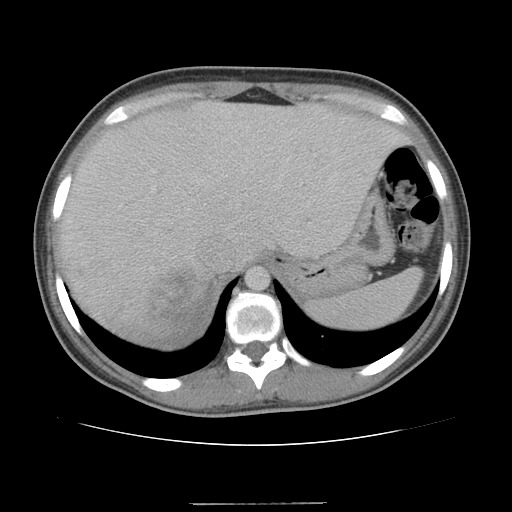
Contrast-enhanced abdominal CT, one axial slice; position 84 of 100 along the scan axis; reconstruction kernel STANDARD; intravenous contrast given; soft-tissue window (W 400 / L 40 HU); 5 mm slice thickness; 512 × 512 image matrix, field of view 360 × 360 mm. Female patient, age 21 years. Case-level facts recorded for this patient, not image findings: diagnosis: adrenocortical carcinoma; tumour side: right adrenal; tumour size at pathology: 15.5 cm; Ki-67 index: 26 %; stage (as recorded): 3.
Structures marked on this image (semi-automatically segmented with operator editing):
- mass: bounding box <150,270,197,317> (left, top, right, bottom; pixels)